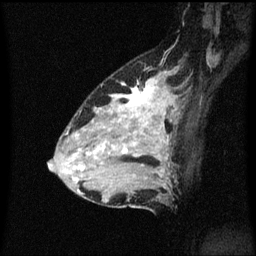
Breast MRI (dynamic contrast-enhanced), one sagittal slice. Position 39 of 60 along the scan axis. Dynamic contrast-enhanced series, image 2 of 3 at this slice position (ordered by acquisition). 1.5 T. TE 4.2 ms, TR 8.4 ms. 2 mm slice thickness. 256 × 256 image matrix. Patient: female, 34 years. Case-level facts recorded for this patient, not image findings: setting: breast cancer imaged before/during neoadjuvant chemotherapy; receptor status: HR-positive, HER2-negative.
Outlined on this slice (semi-automatically segmented with operator editing):
- analysis volume of interest (the breast-tissue region the enhancement analysis was run in; not a lesion): box from (x=69, y=72) to (x=178, y=209) px
- tumour enhancement mask (voxels above the 70 % enhancement threshold inside the analysis volume of interest): (x=72, y=80)–(x=173, y=181)